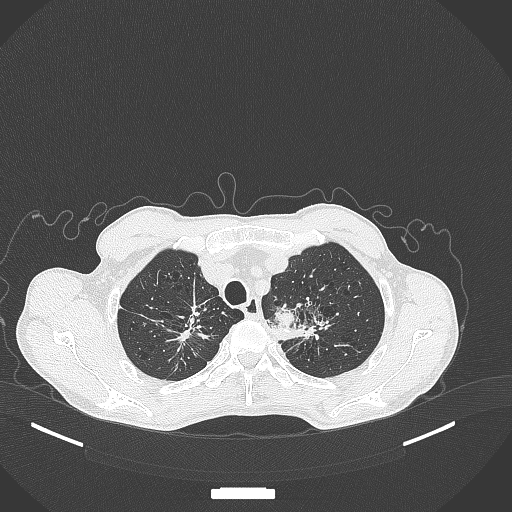
Chest CT, one axial slice. Slice 363 of 386 in the series (ordered by position). Reconstruction kernel B70f. Lung window (W 1500 / L -600 HU). 1 mm slice thickness. 512 × 512 image matrix, field of view 400 × 400 mm. Patient: male, 65 years. Case-level facts recorded for this patient, not image findings: clinical TNM (as recorded): T2b N0 M0.
Structures marked on this image (bounding box drawn by a radiologist):
- lung tumour (recorded histology: adenocarcinoma): bounding box [x1, y1, x2, y2] px = [269, 300, 299, 332]